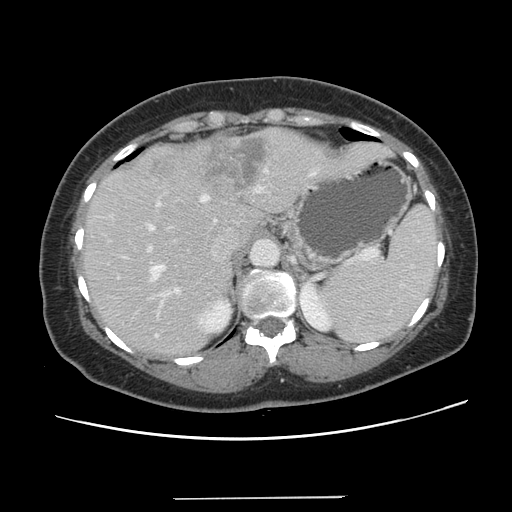
Contrast-enhanced abdominal CT, one axial slice; position 95 of 141 along the scan axis; intravenous contrast given; soft-tissue window (W 400 / L 40 HU); 2.5 mm slice thickness; 512 × 512 image matrix. Female patient, age 53 years. Case-level facts recorded for this patient, not image findings: diagnosis: colorectal cancer liver metastases, imaged before liver resection; multiple liver metastases: no; largest metastasis: 14.5 cm.
Structures marked on this image (manually delineated by an expert):
- hepatic veins: bounding box (x1, y1, x2, y2) in pixels: (150, 168, 318, 280)
- liver: (84, 129, 389, 355)
- planned liver remnant (the part of the liver to remain after resection): (84, 210, 262, 355)
- portal vein (with intrahepatic branches): (146, 187, 261, 318)
- liver metastasis: (201, 138, 267, 190)